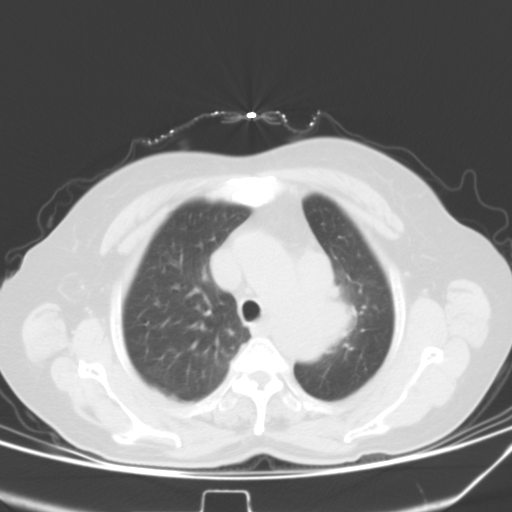
Chest CT, one axial slice; position 34 of 42 along the scan axis; 120 kVp; lung window (W 1500 / L -600 HU); 5 mm slice thickness; 512 × 512 image matrix. Patient: female, 59 years. From the clinical record (not read from this slice): clinical TNM (as recorded): T3 N1 M0; histopathological grade: G3.
Annotated regions visible in this slice (rectangle marked by the reading radiologist):
- lung tumour (recorded histology: small cell carcinoma): bounding box [x1, y1, x2, y2] px = [326, 285, 360, 353]